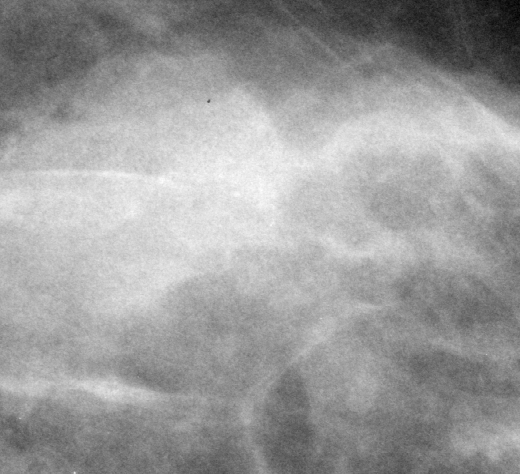
Cropped region of a digitized screen-film mammogram centred on a radiologist-marked abnormality, left breast, MLO view, BI-RADS breast density category 1 (scale 1–4).
Marked abnormality: mass, shape oval, margins ill defined; BI-RADS assessment category 3; subtlety rating 5 on a 1 (subtle) to 5 (obvious) scale; benign; no additional work-up was recommended (benign without callback).